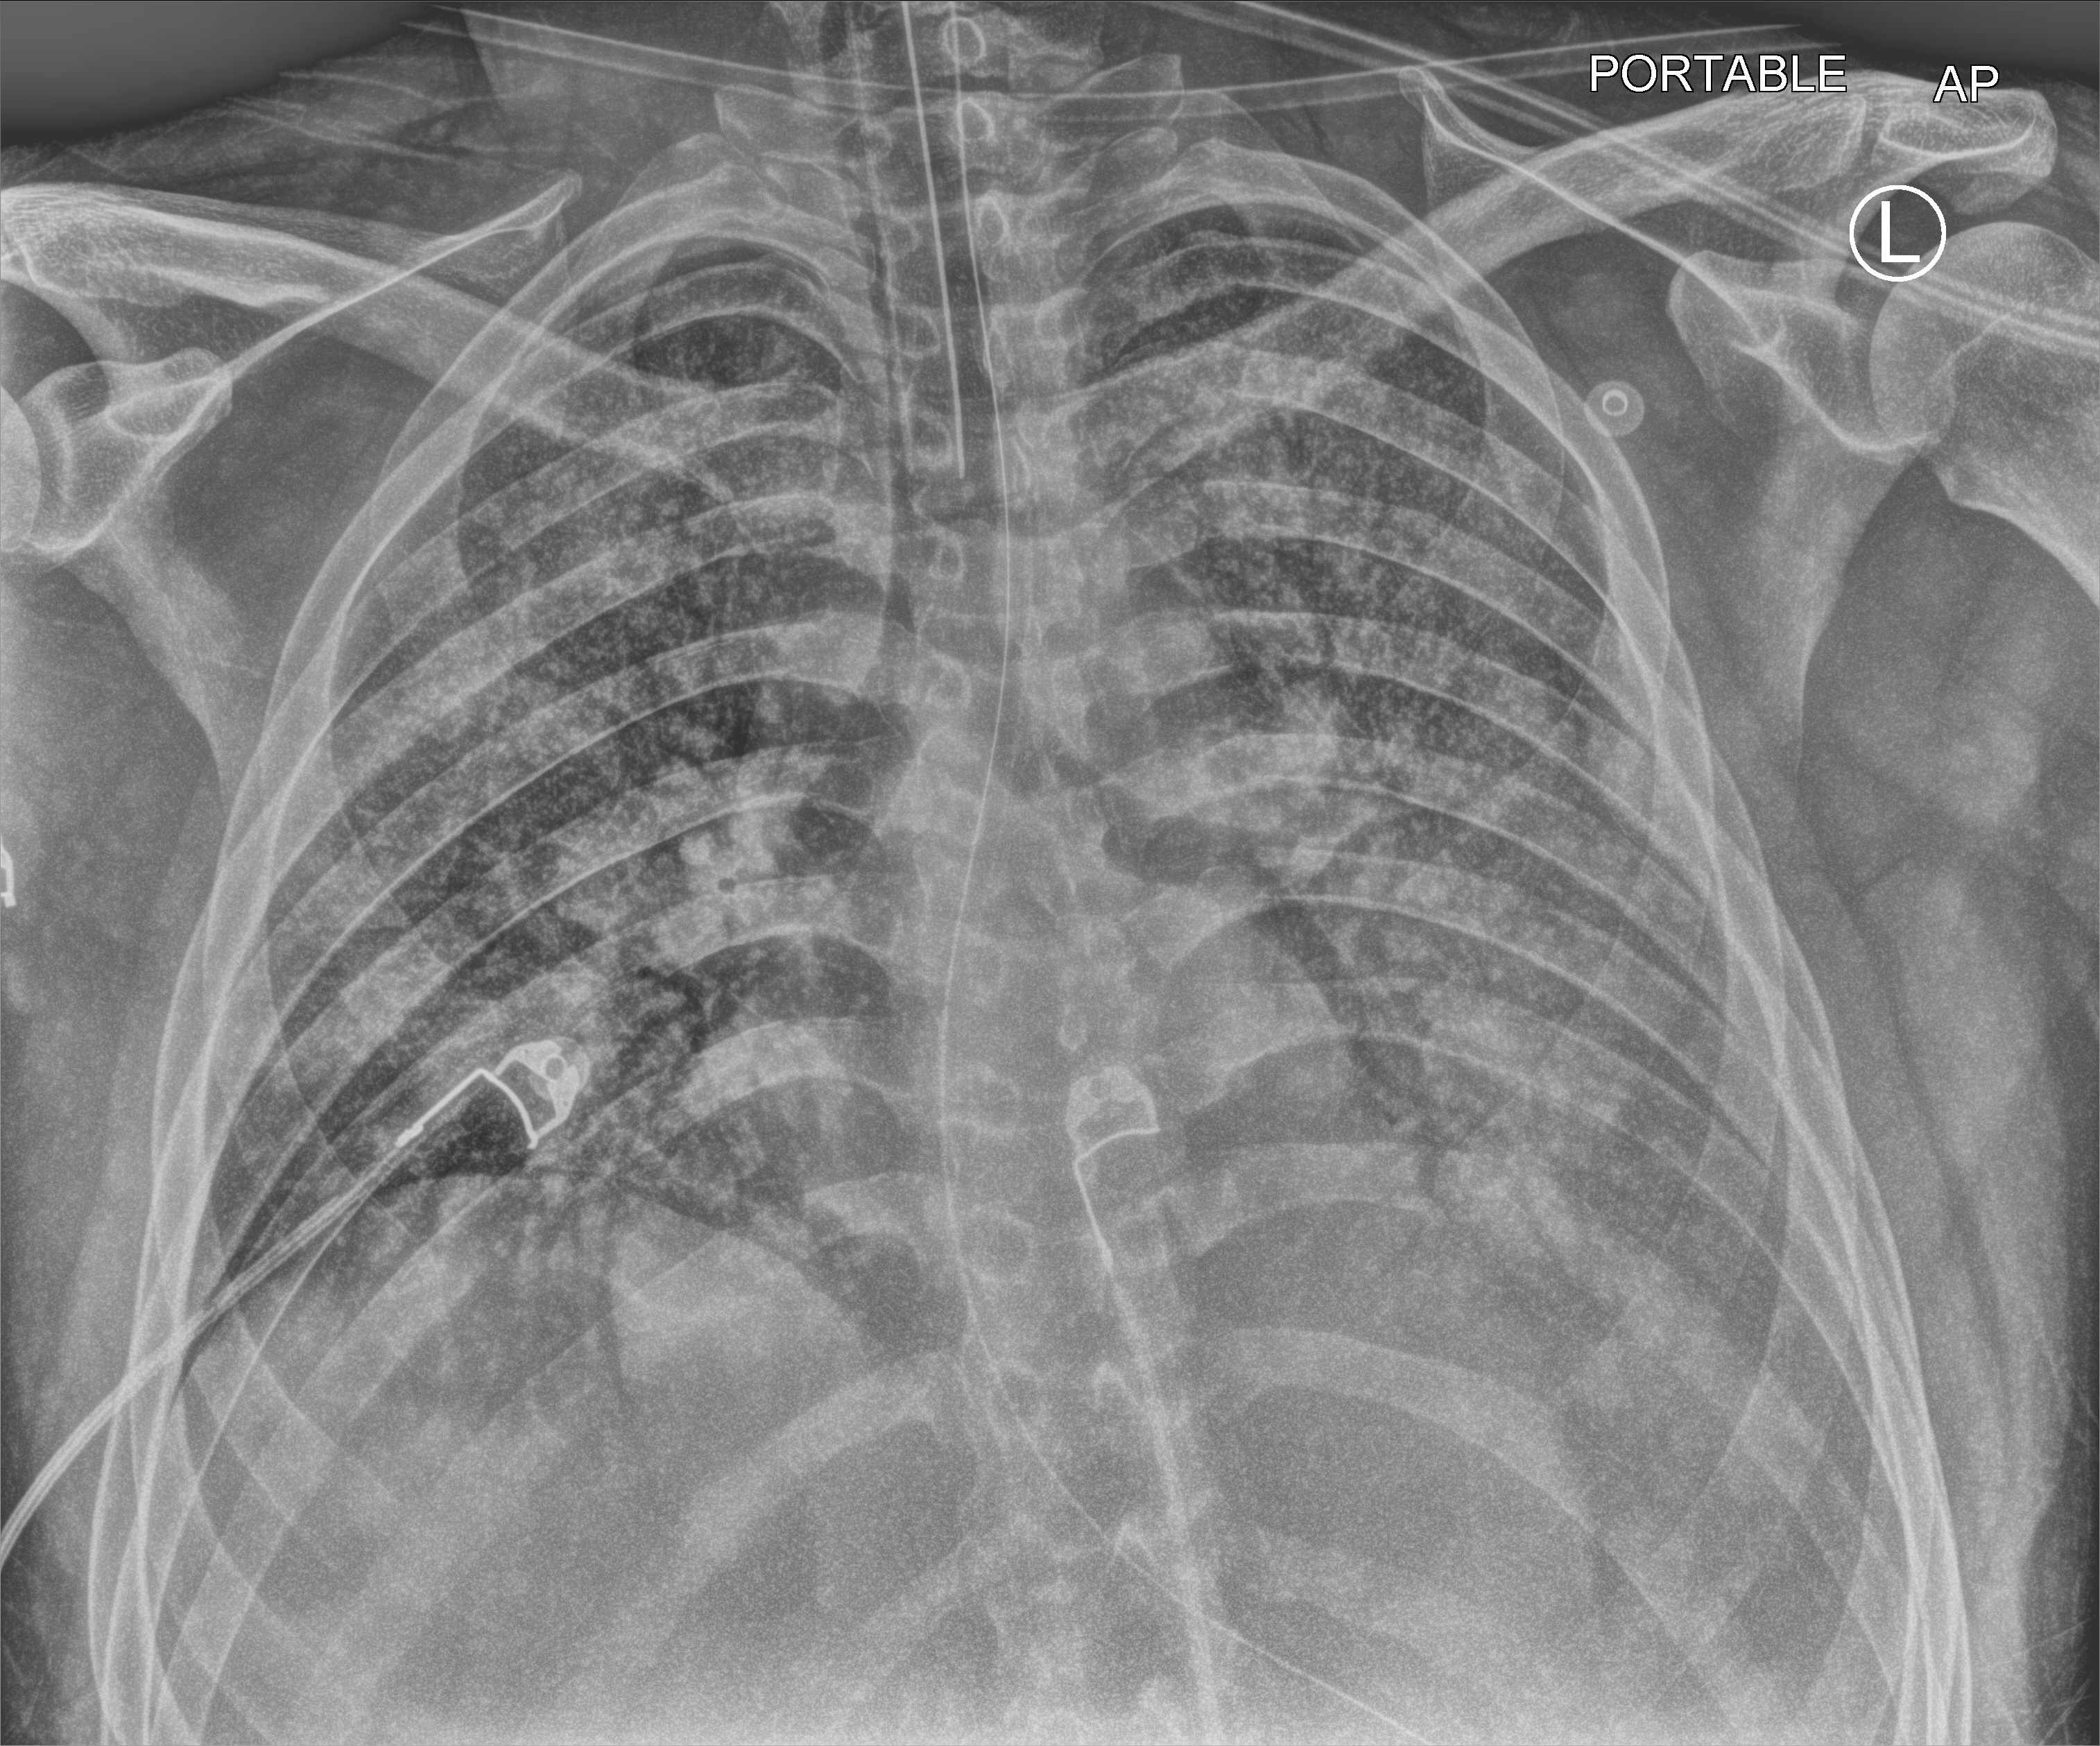
Portable chest radiograph. Male patient hospitalised with COVID-19, age 18–59 years.
Admission-level facts for this patient (not findings on this image; timing relative to this image not recorded): length of hospital stay: 61 days; chronic kidney disease (admission record): no.